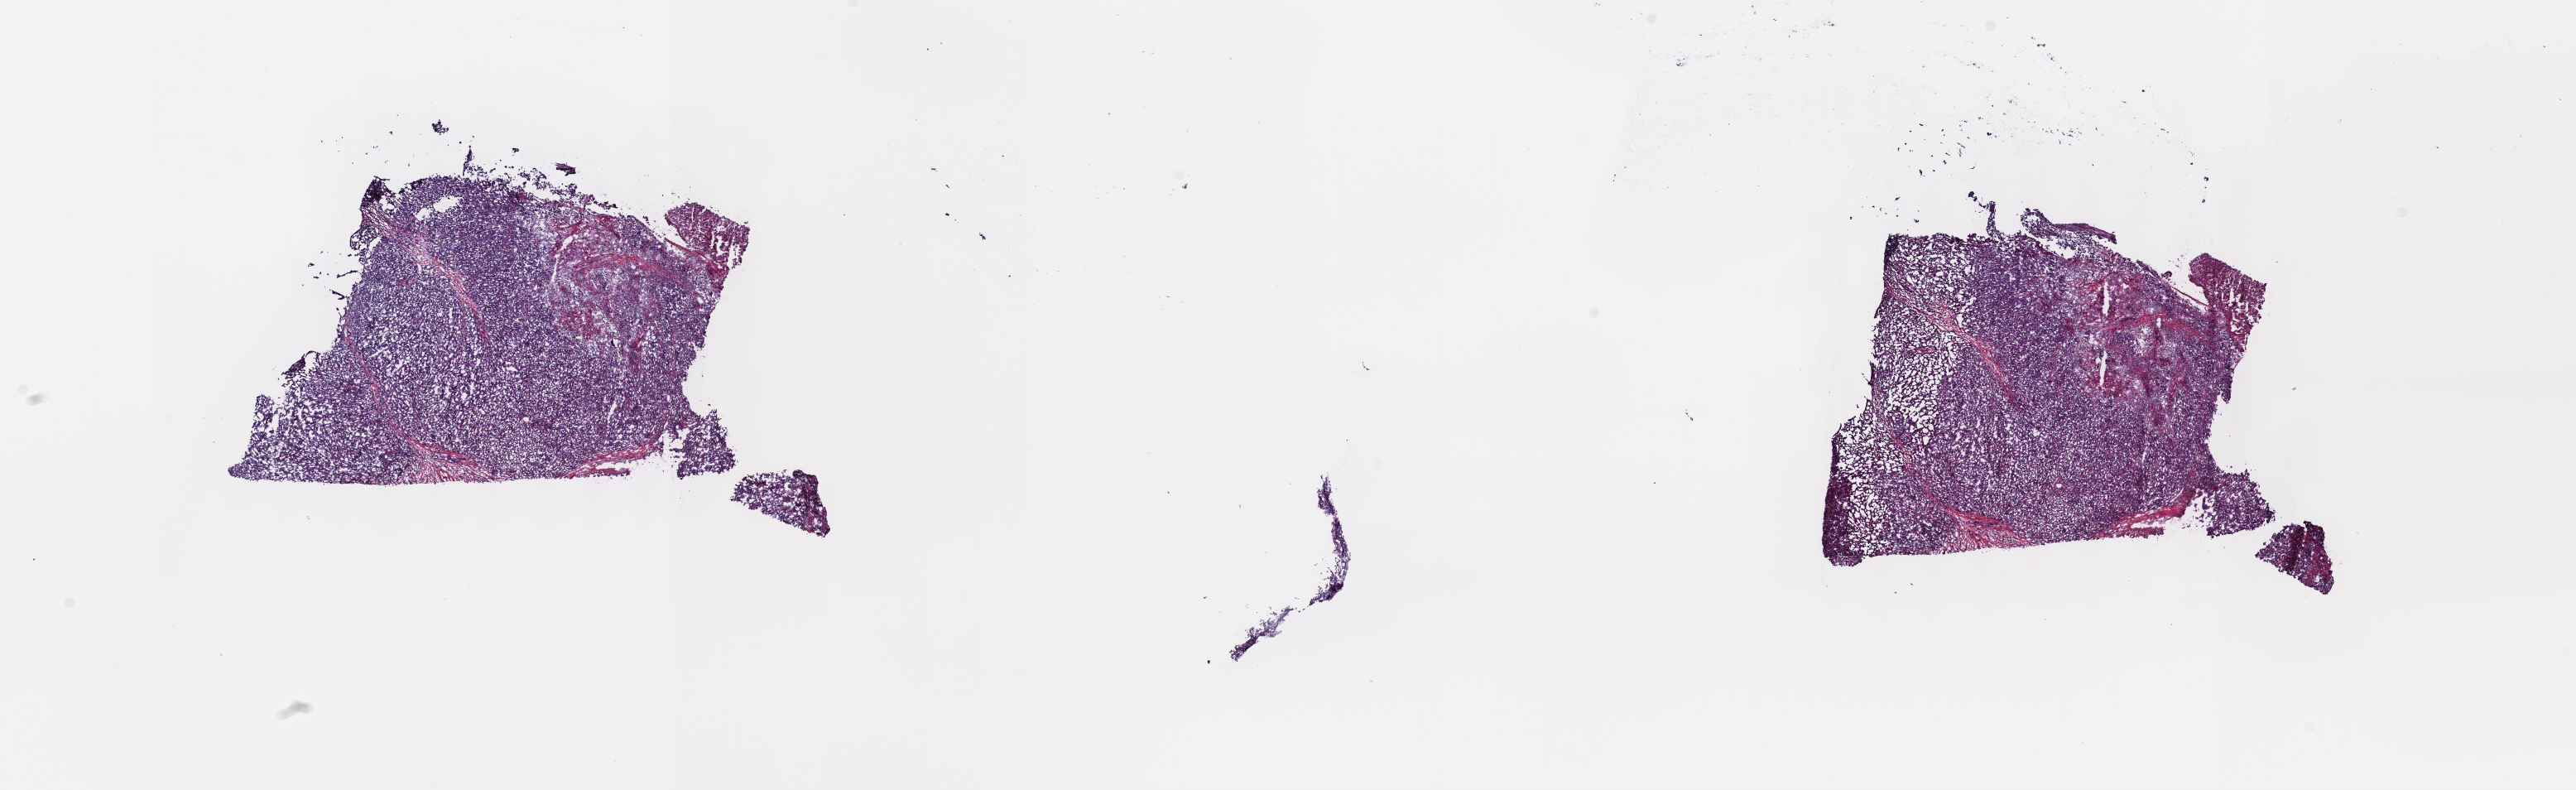
Whole-slide histology image, H&E — whole scanned area (about 25.2 x 7.7 mm, from a 40x scan) shown as a low-resolution overview, frozen section from the top of the tissue portion, metastatic tumour sample, sampled site: connective, subcutaneous and other soft tissues of lower limb and hip. Patient: male, age at initial diagnosis 74 years.
This section: metastatic tumour tissue. Patient diagnosis: Superficial spreading melanoma.